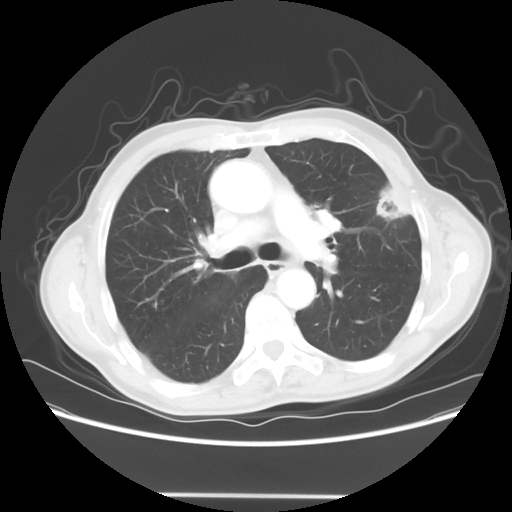
Chest CT, one axial slice; position 39 of 64 along the scan axis; 120 kVp; lung window (W 1500 / L -600 HU); 512 × 512 image matrix, field of view 392 × 392 mm. Male patient, age 71 years. Case-level facts recorded for this patient, not image findings: clinical TNM (as recorded): T1c N0 M0; histopathological grade: G2-3.
Annotated regions visible in this slice (rectangle marked by the reading radiologist):
- lung tumour (recorded histology: adenocarcinoma): box from (x=370, y=174) to (x=420, y=232) px